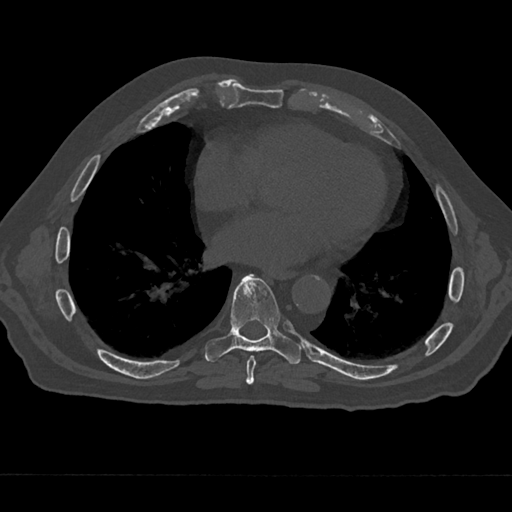
CT including the spine, one axial slice; slice 326 of 797 in the series (ordered by position); reconstruction kernel Br40s/3; bone window (W 1800 / L 400 HU); 512 × 512 image matrix. Patient: male, 75 years. From the clinical record (not read from this slice): primary cancer: renal; vertebrae with lytic lesions (as recorded): T4.
Annotated regions visible in this slice (semi-automatic segmentation, software-assisted and operator-edited):
- T7 vertebra: bounding box (x1, y1, x2, y2) in pixels: (243, 355, 257, 385)
- T8 vertebra: (204, 274, 301, 364)